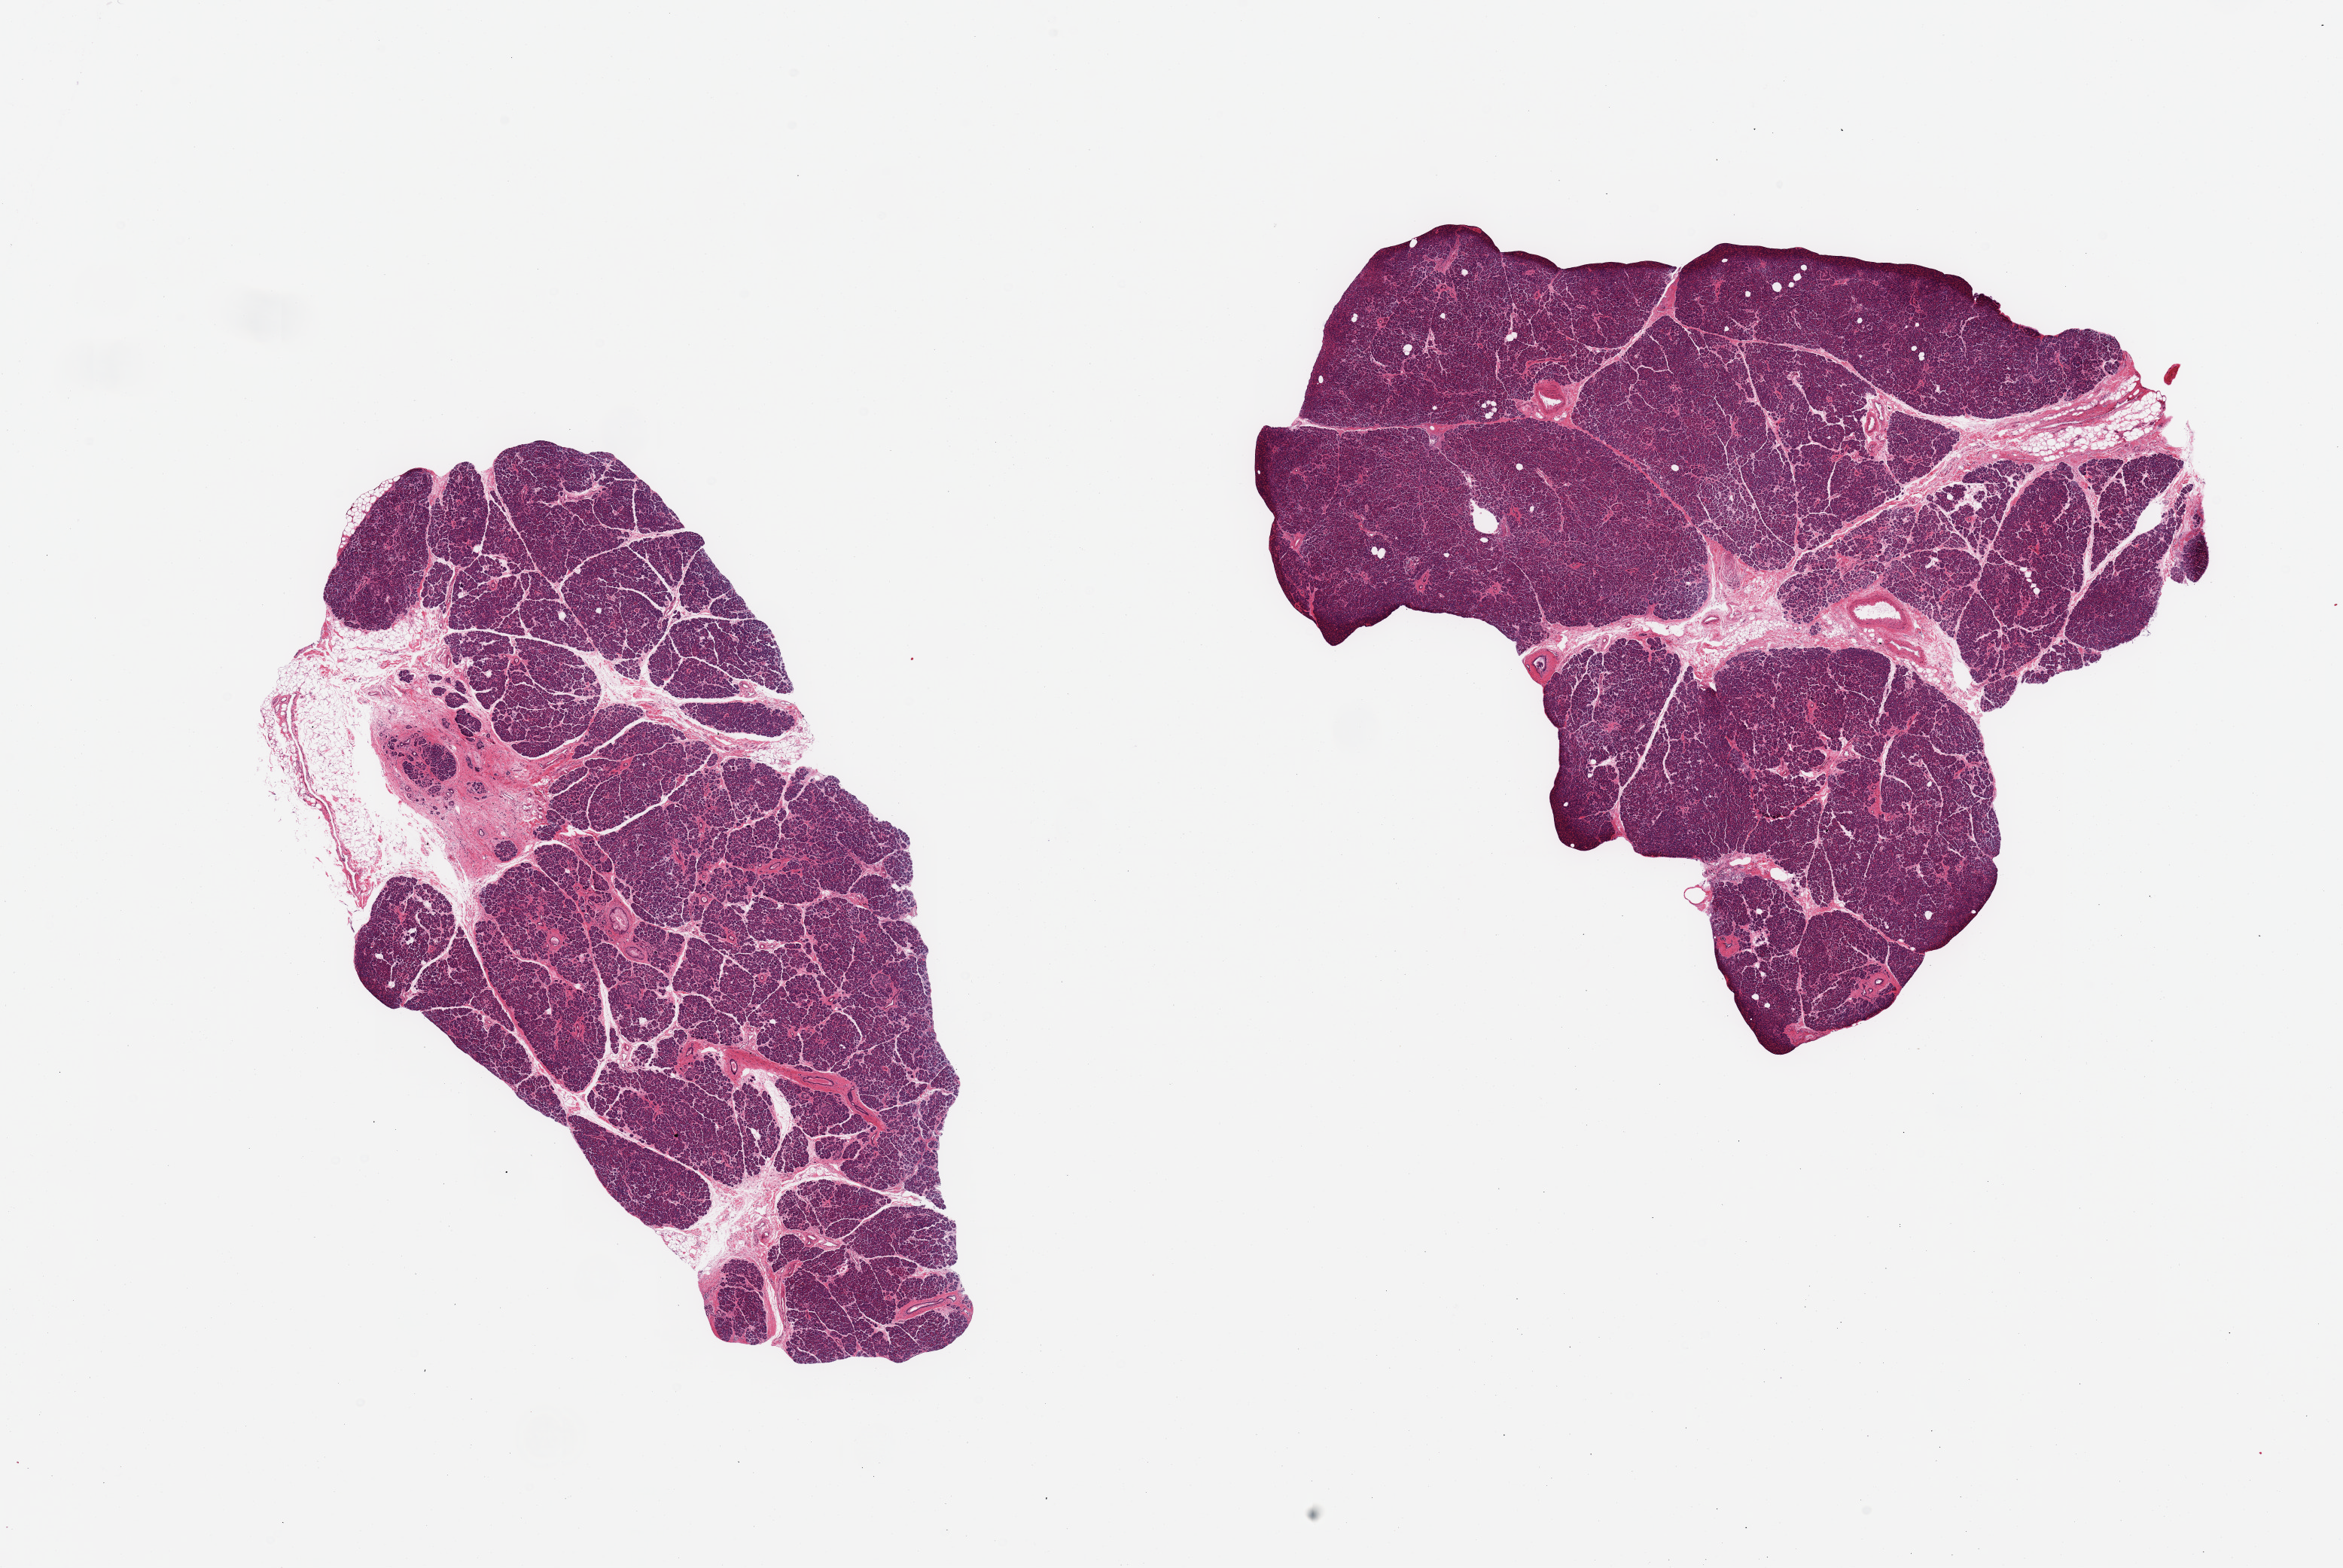
Digitized H&E-stained section, brightfield, whole scanned area (about 24.6 x 16.5 mm) shown as a low-resolution overview. Donor sex: female.
Specimen: PAXgene-fixed, paraffin-embedded tissue; section of pancreas (target tissue); tissue donor sample.